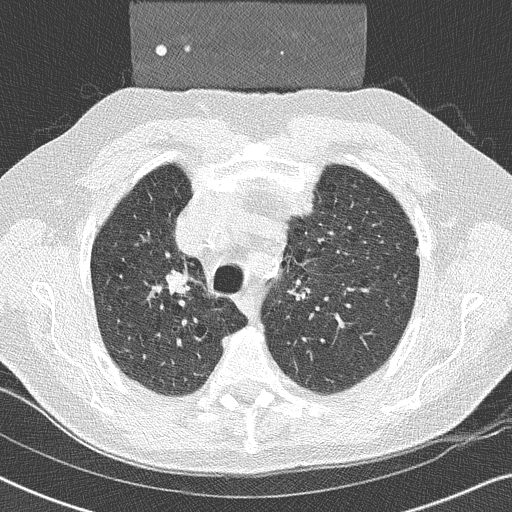
Low-dose screening chest CT, one axial slice; position 182 of 252 along the scan axis; reconstruction kernel B50f; lung window (W 1500 / L -600 HU); 2 mm slice thickness; 512 × 512 image matrix, field of view 330 × 330 mm.
Structures marked on this image (expert manual segmentation):
- lesion 1 (tumor, upper lobe of right lung): bounding box (x1, y1, x2, y2) in pixels: (168, 271, 187, 294)